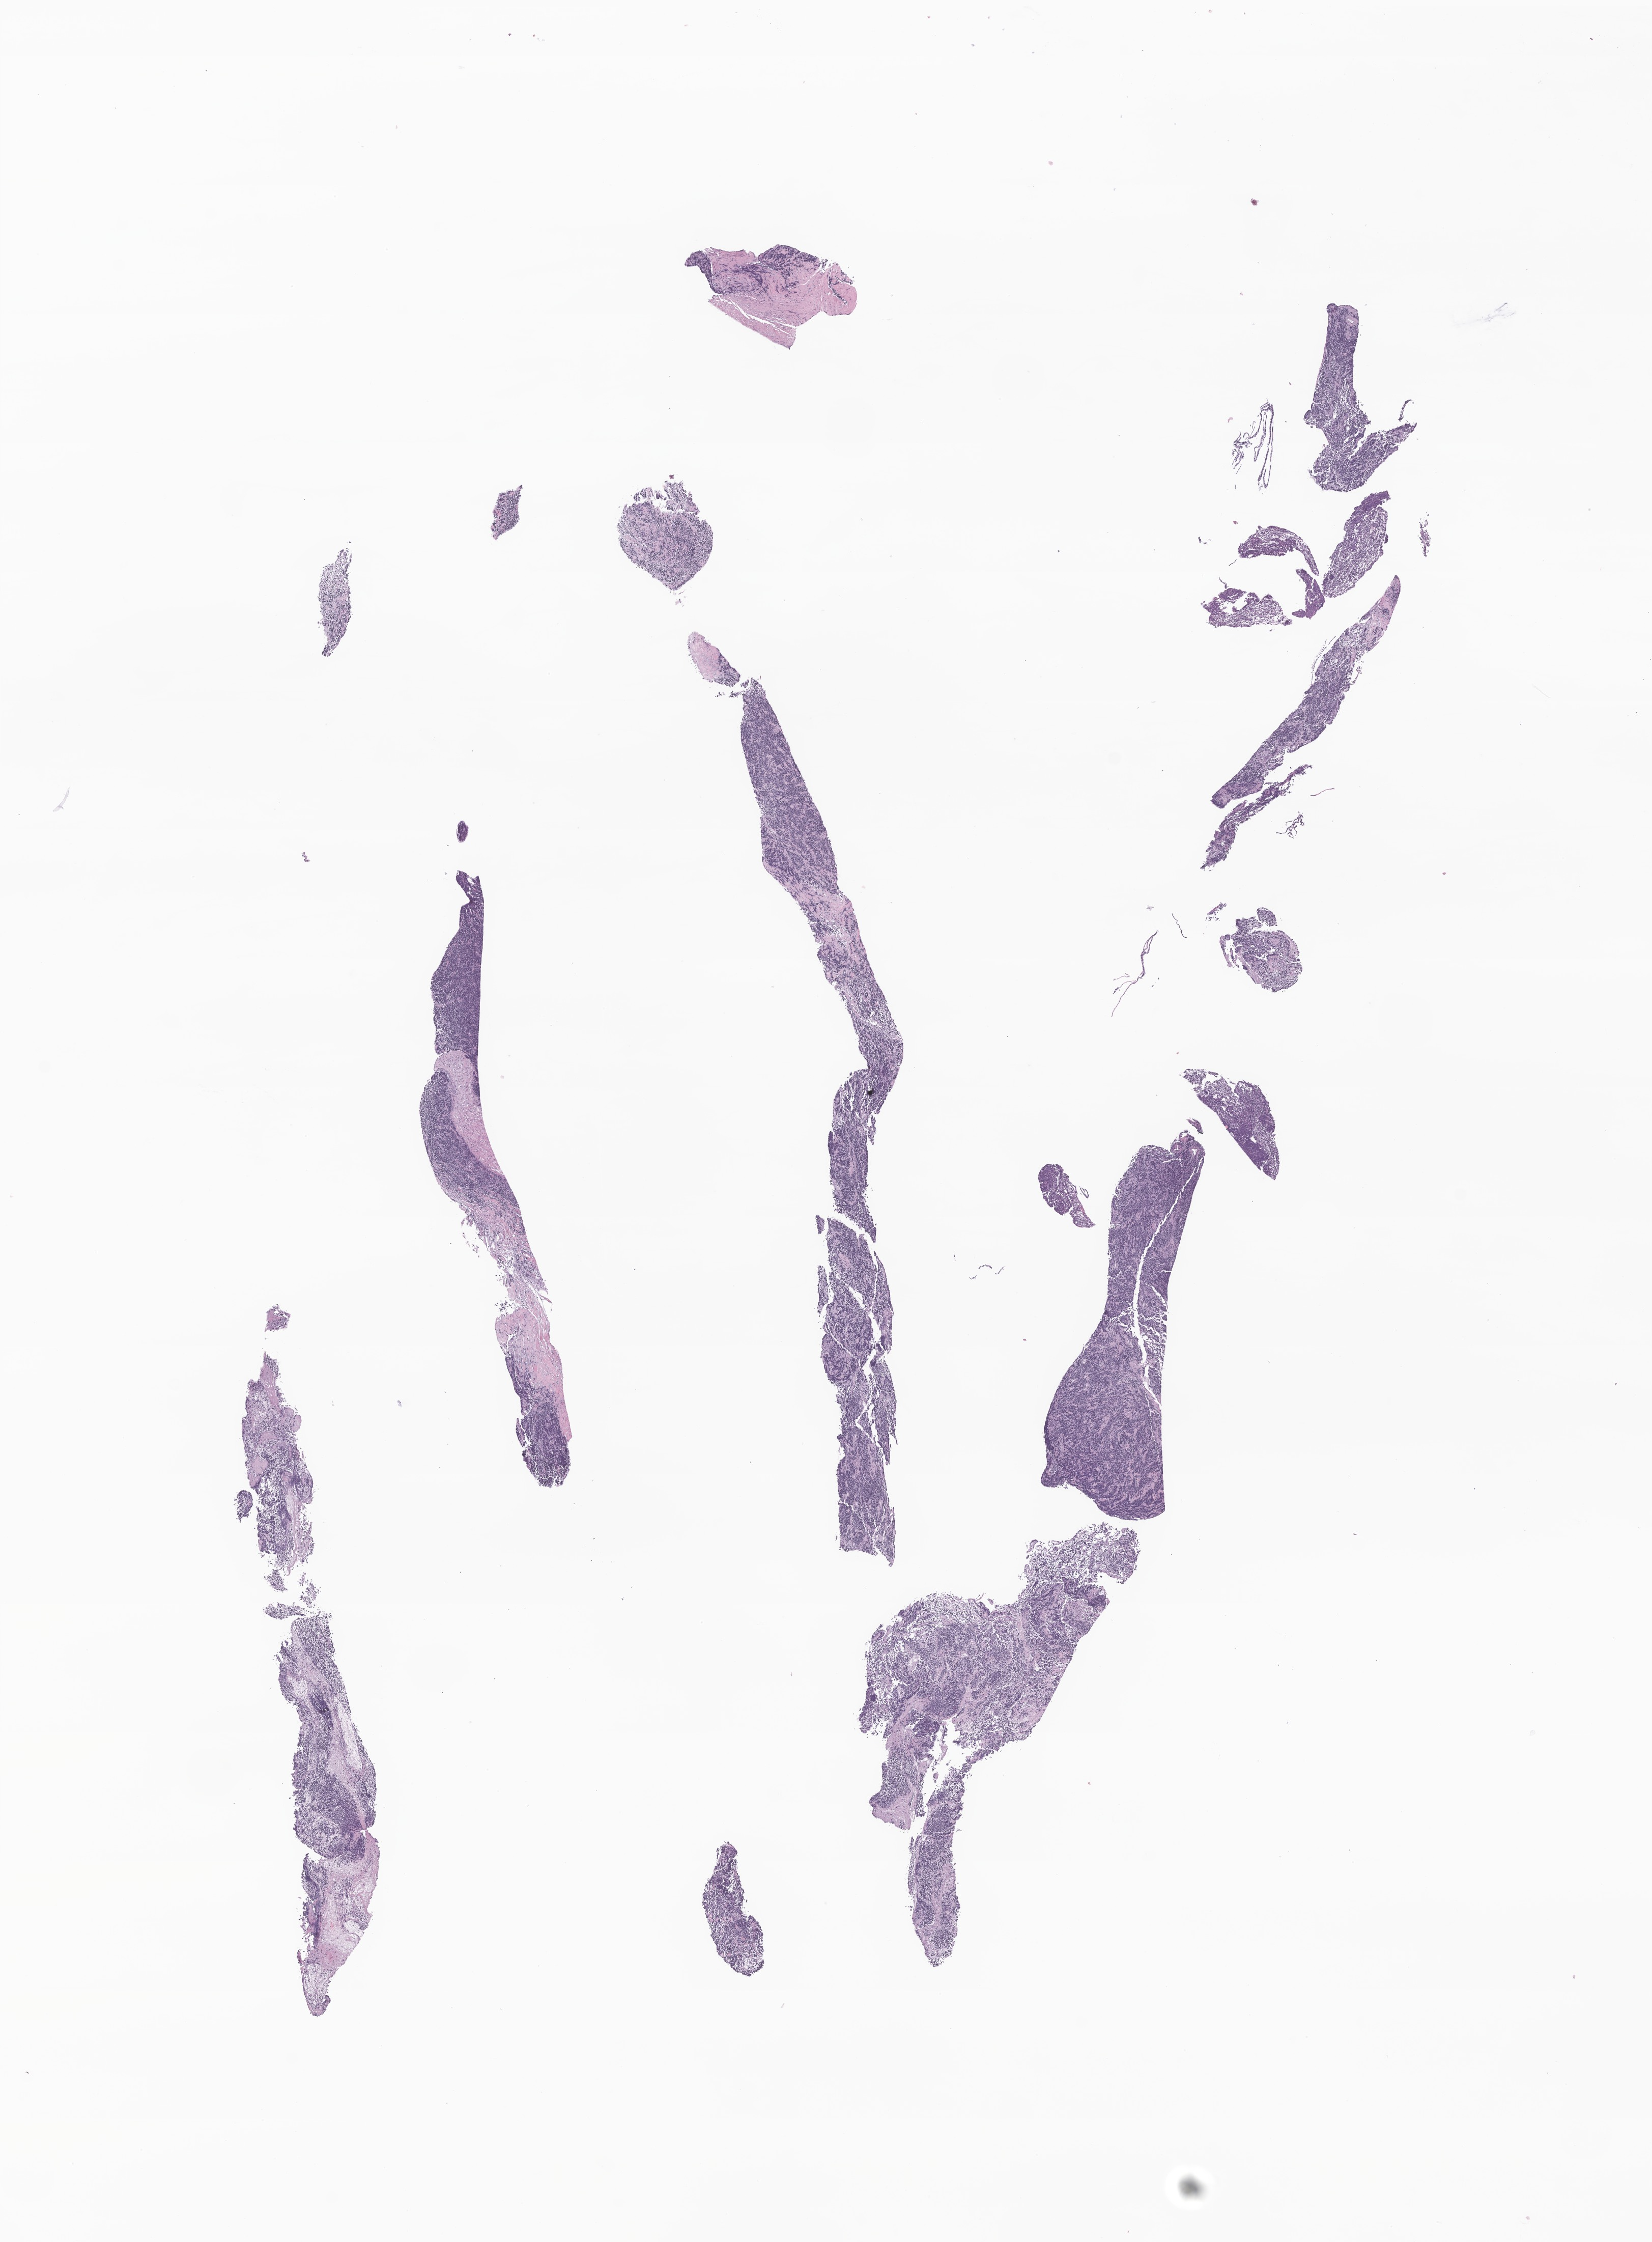
Whole-slide image, hematoxylin and eosin (H&E) stain of tumor tissue from the posterior mediastinum, shown as a low-resolution overview of the whole scanned area (about 13.7 x 18.6 mm), FFPE section. Patient female; age 79 months.
Diagnosis (ICD-O-3 morphology term): Neuroblastoma, NOS.